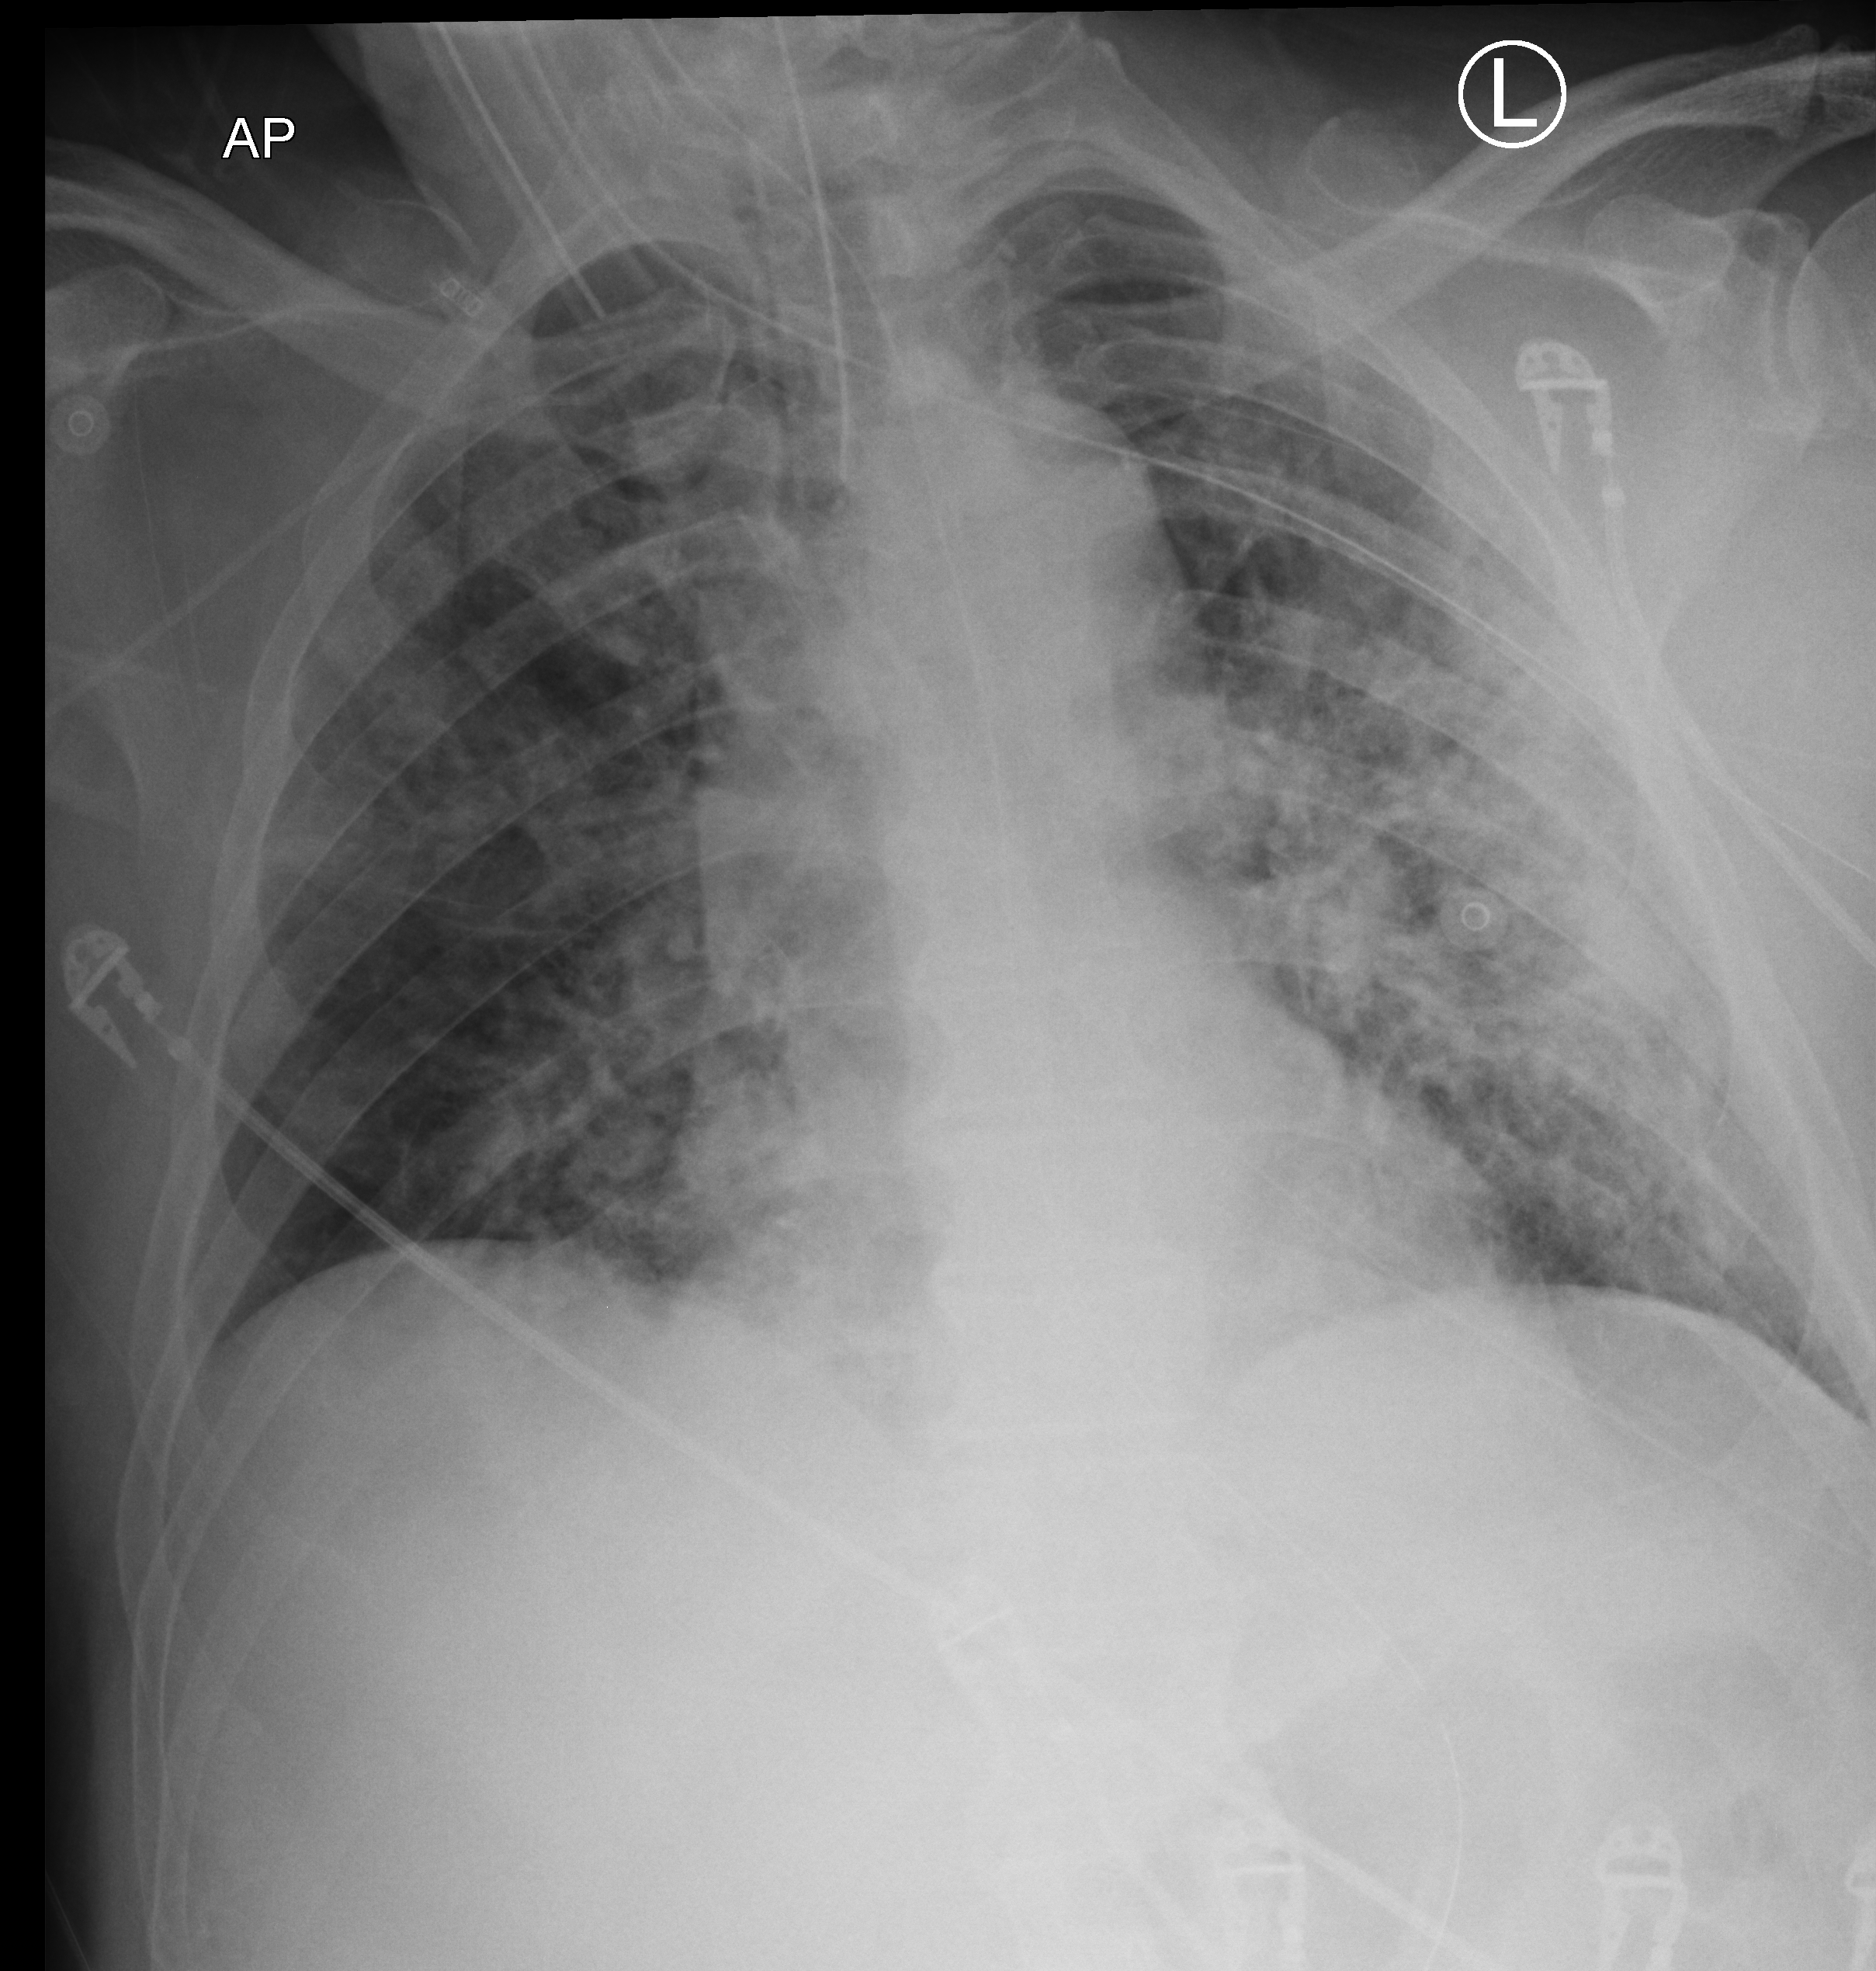
Bedside chest radiograph (computed radiography), anteroposterior (AP) projection. Male patient hospitalised with COVID-19, age 60–74 years.
Hospital-stay facts (about this admission, not read from this image; timing relative to this image not recorded):
- admitted to intensive care during this hospital stay: yes